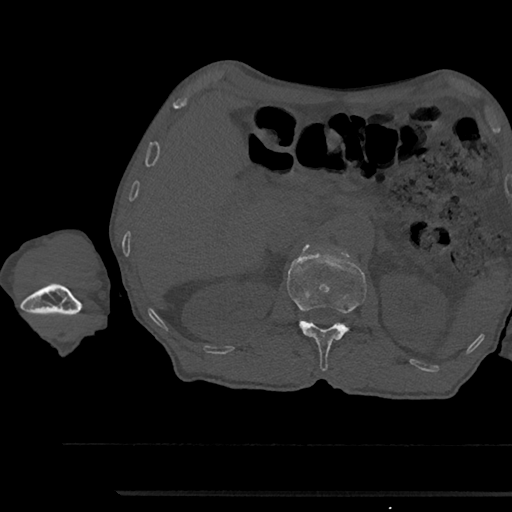
CT including the spine, one axial slice. Slice 631 of 797 in the series (ordered by position). 120 kVp. Bone window (W 1800 / L 400 HU). 0.5 mm slice thickness. 512 × 512 image matrix. Male patient, age 79 years. From the clinical record (not read from this slice): primary cancer: prostate.
Annotated regions visible in this slice (semi-automatic segmentation, software-assisted and operator-edited):
- L1 vertebra: bounding box <287,245,367,371> (left, top, right, bottom; pixels)